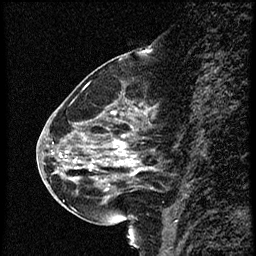
Breast MRI (dynamic contrast-enhanced), one sagittal slice; slice 24 of 56 in the series (ordered by position); dynamic contrast-enhanced study with each time point stored as its own series, time point 2 of 4 at this slice position (early post-contrast, ordered by acquisition time); 1.5 T; TE 4.2 ms, TR 18.9 ms; 2 mm slice thickness; 256 × 256 image matrix. Female patient. Case-level facts recorded for this patient, not image findings: setting: breast cancer imaged before/during neoadjuvant chemotherapy; receptor status: HER2-positive.
Outlined on this slice (semi-automatic segmentation, software-assisted and operator-edited):
- analysis volume of interest (the breast-tissue region the enhancement analysis was run in; not a lesion): bounding box <63,80,156,215> (left, top, right, bottom; pixels)
- tumour enhancement mask (voxels above the 100 % enhancement threshold inside the analysis volume of interest): <67,112,143,175>